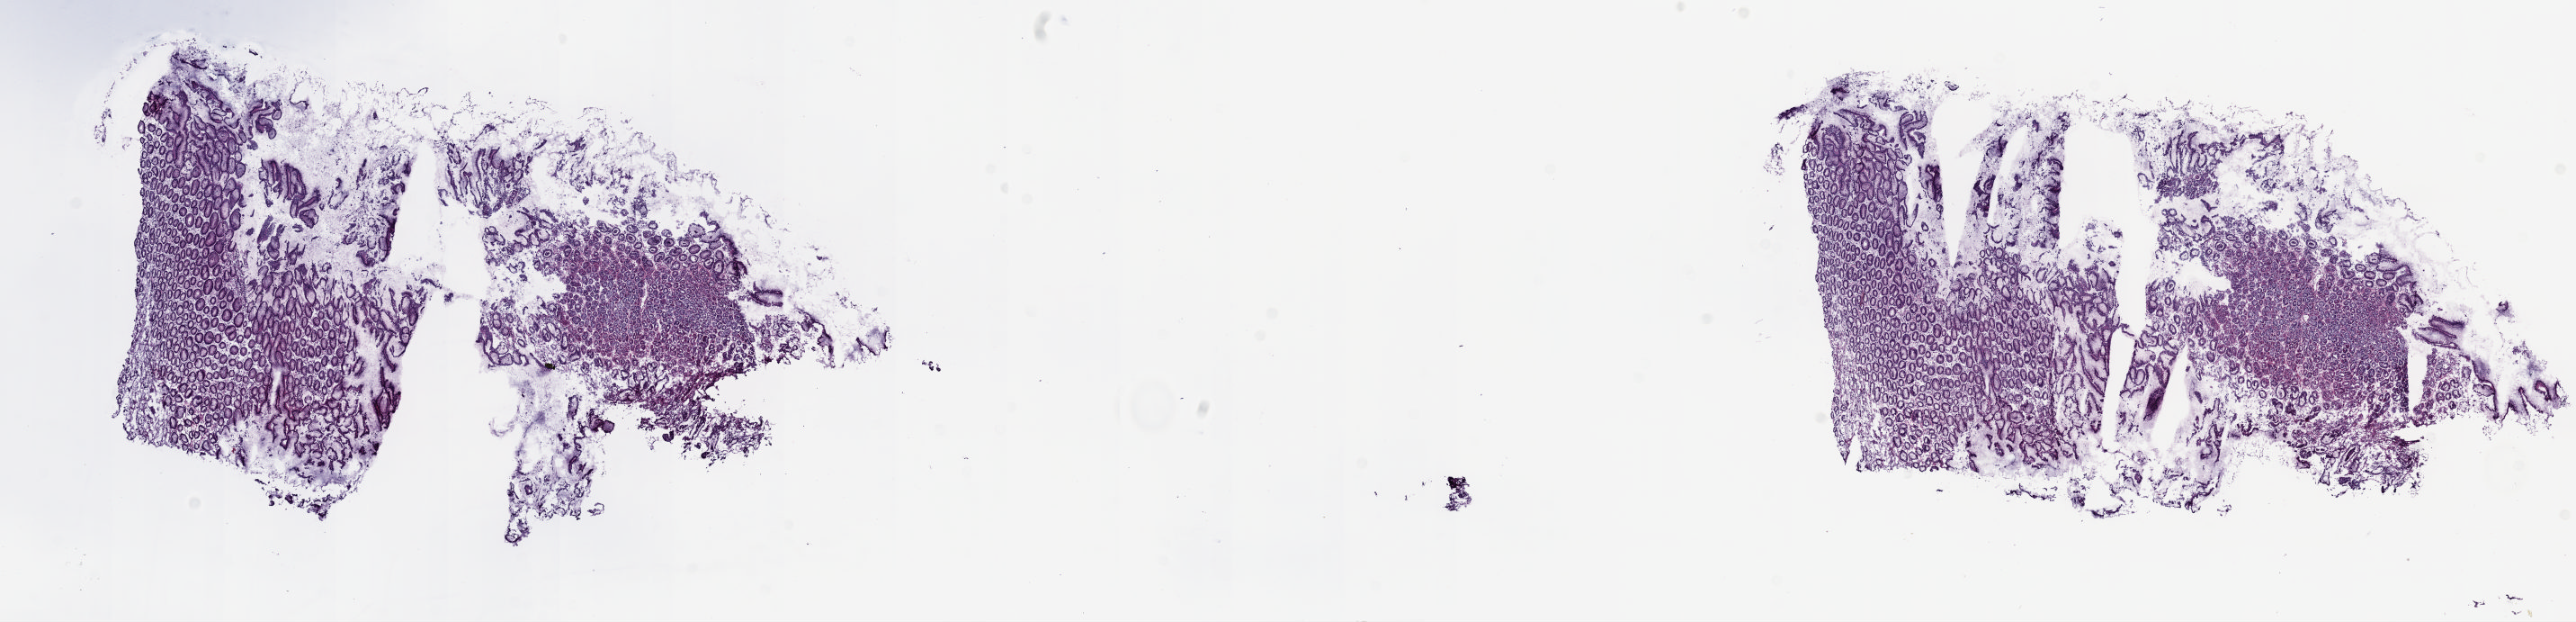
H&E whole-slide image — shown as a low-resolution overview of the whole scanned area (about 23.1 x 5.6 mm, from a 20x scan); frozen section; esophagus, solid tissue normal (non-tumour tissue) sample. Male patient; age at initial diagnosis 77 years. Pathologist review of this section (percent, as recorded): tumour cells 0%, tumour nuclei 0%, normal cells 100%, stromal cells 0%, necrosis 0%. Infiltration values recorded for this section: lymphocyte infiltration 5%, monocyte infiltration 0%, neutrophil infiltration 0%.
* this section: solid tissue normal sample (biorepository sample class)
* patient diagnosis: Adenocarcinoma, NOS (lower third of esophagus)